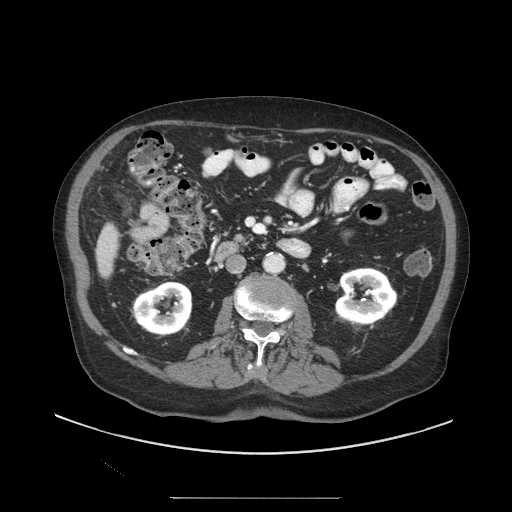
Contrast-enhanced abdominal CT (liver protocol), one axial slice. Slice 30 of 97 in the series (ordered by position). 140 kVp. Soft-tissue window (W 400 / L 40 HU). 2.5 mm slice thickness. 512 × 512 image matrix. From the clinical record (not read from this slice): diagnosis: hepatocellular carcinoma (patient treated with transarterial chemoembolisation; whether this scan precedes or follows treatment is not stated here); TNM stage (as recorded): Stage-IIIC; Child-Pugh class: A; tumour nodularity: uninodular; tumour size: 9.2 cm.
Structures marked on this image (semi-automatic segmentation, software-assisted and operator-edited):
- liver parenchyma outside the tumour (the mass and vessels are separate outlines, so this box may not span the whole liver): bounding box <96,223,118,278> (left, top, right, bottom; pixels)